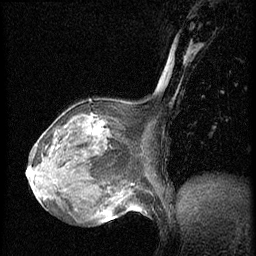
Breast MRI (dynamic contrast-enhanced), one sagittal slice; slice 26 of 56 in the series (ordered by position); dynamic contrast-enhanced series, image 2 of 3 at this slice position (ordered by acquisition); 1.5 T; TE 4.2 ms, TR 20.4 ms; 2 mm slice thickness; 256 × 256 image matrix, field of view 200 × 200 mm. Female patient, age 64 years. From the clinical record (not read from this slice): setting: breast cancer imaged before/during neoadjuvant chemotherapy; receptor status: HR-positive, HER2-negative.
Annotated regions visible in this slice (semi-automatically segmented with operator editing):
- analysis volume of interest (the breast-tissue region the enhancement analysis was run in; not a lesion): bounding box <48,101,138,186> (left, top, right, bottom; pixels)
- tumour enhancement mask (voxels above the 70 % enhancement threshold inside the analysis volume of interest): <87,117,103,136>